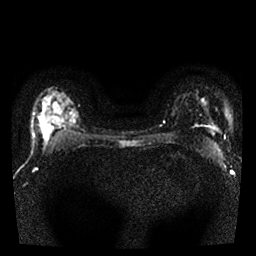
Breast MRI, one axial slice. Position 18 of 25 along the scan axis. Diffusion-weighted series; image 2 of 4 stored at this slice position (different b-values; order by instance number). 1.5 T. 4 mm slice thickness. 256 × 256 image matrix. Female patient.
Outlined on this slice (expert manual segmentation):
- tumour on diffusion-weighted imaging: bounding box <40,120,50,134> (left, top, right, bottom; pixels)